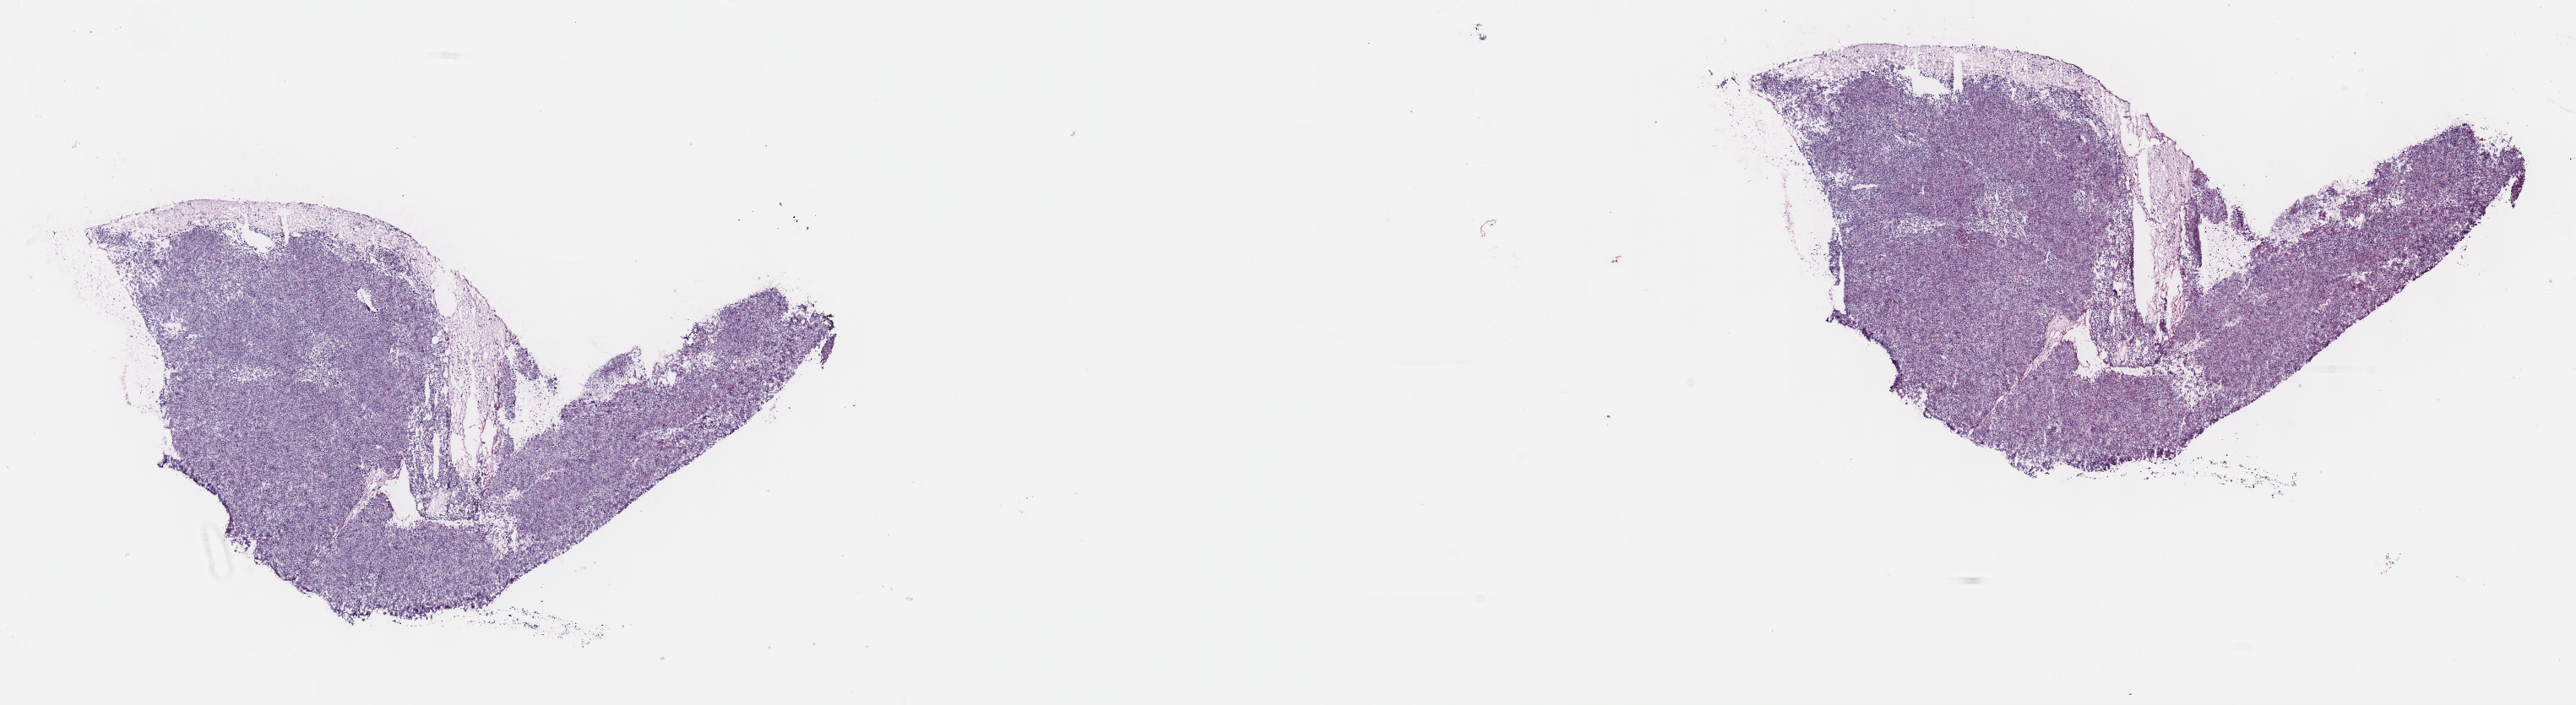
Hematoxylin and eosin (H&E) stained whole-slide image — a low-resolution overview of the entire scanned area, about 24.7 x 6.8 mm (acquisition: 40x scan), frozen section from the top of the tissue portion, lymphoid tissue, primary tumour sample. Patient: male, age at initial diagnosis 74 years.
Diagnosis: Diffuse large B-cell lymphoma, NOS (lymph nodes of head, face and neck).